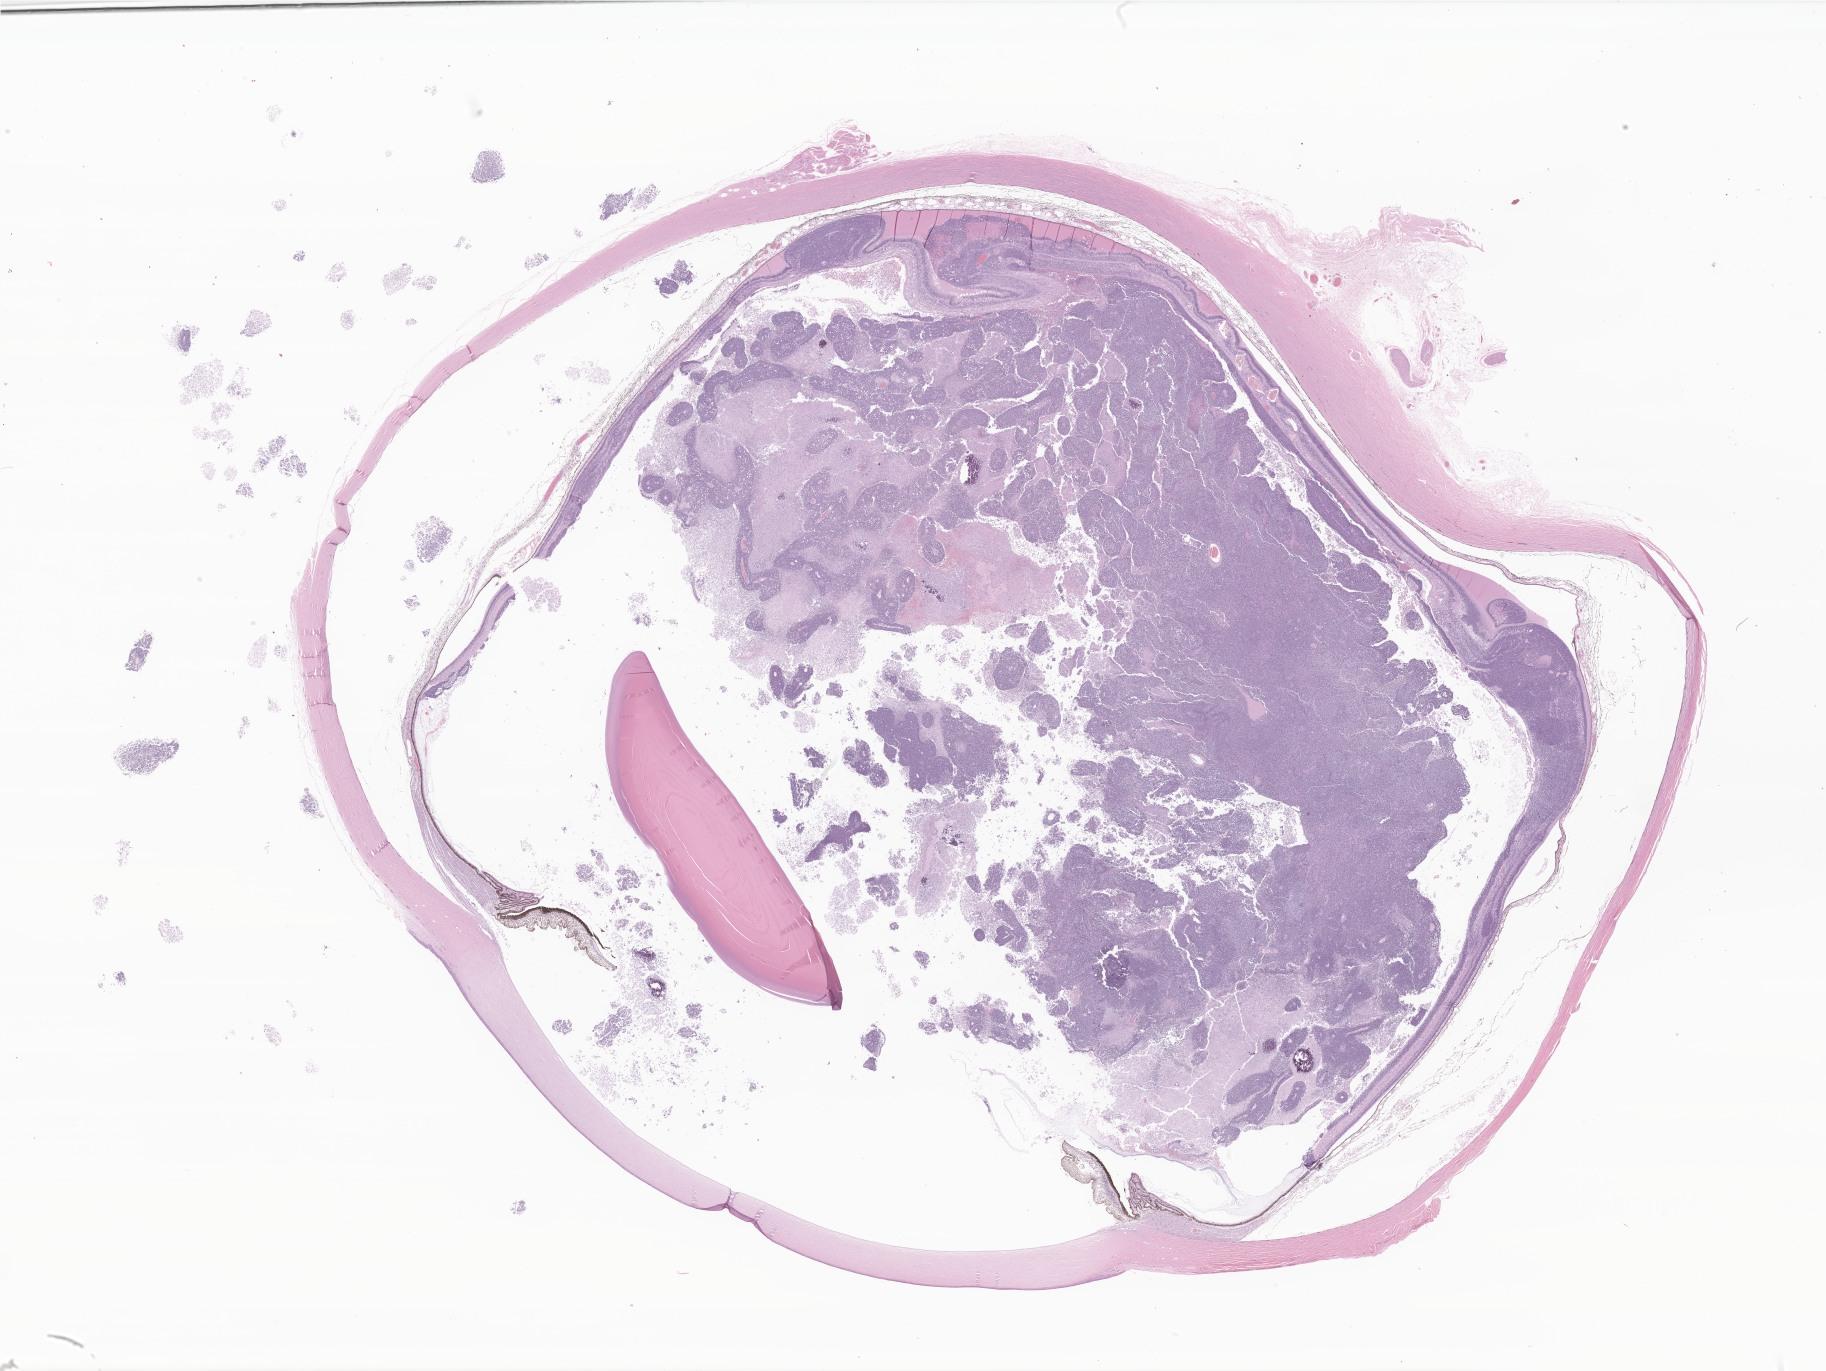
Hematoxylin and eosin (H&E) whole-slide image of tumor tissue from the eye, whole scanned area (about 30.8 x 23.1 mm) shown as a low-resolution overview; formalin-fixed paraffin-embedded section. Male patient, age 42 months (3 years 6 months).
Recorded diagnosis: Retinoblastoma, NOS.